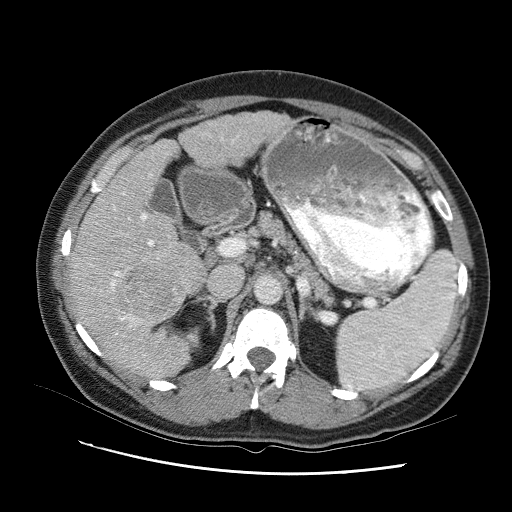
Contrast-enhanced abdominal CT (liver protocol), one axial slice; slice 54 of 95 in the series (ordered by position); reconstruction kernel STANDARD; 120 kVp; one of 2 acquisitions stored at this slice position; soft-tissue window (W 400 / L 40 HU); 2.5 mm slice thickness; 512 × 512 image matrix, field of view 360 × 360 mm. From the clinical record (not read from this slice): diagnosis: hepatocellular carcinoma (patient treated with transarterial chemoembolisation; whether this scan precedes or follows treatment is not stated here); TNM stage (as recorded): Stage-I; Child-Pugh class: B; tumour nodularity: uninodular.
Structures marked on this image (semi-automatically segmented with operator editing):
- liver parenchyma outside the tumour (the mass and vessels are separate outlines, so this box may not span the whole liver): bounding box <66,106,294,376> (left, top, right, bottom; pixels)
- mass: <124,263,178,310>
- liver vessels: <97,121,237,352>